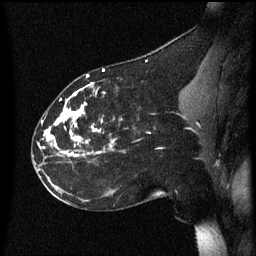
Breast MRI (dynamic contrast-enhanced), one sagittal slice; position 28 of 60 along the scan axis; dynamic contrast-enhanced series, image 2 of 3 at this slice position (ordered by acquisition); 1.5 T; TE 4.2 ms, TR 8.4 ms; 256 × 256 image matrix. Patient: female, 35 years. Case-level facts recorded for this patient, not image findings: setting: breast cancer imaged before/during neoadjuvant chemotherapy; receptor status: HER2-positive.
Outlined on this slice (semi-automatic segmentation, software-assisted and operator-edited):
- analysis volume of interest (the breast-tissue region the enhancement analysis was run in; not a lesion): bounding box [x1, y1, x2, y2] px = [32, 72, 157, 173]
- tumour enhancement mask (voxels above the 70 % enhancement threshold inside the analysis volume of interest): [40, 74, 116, 157]